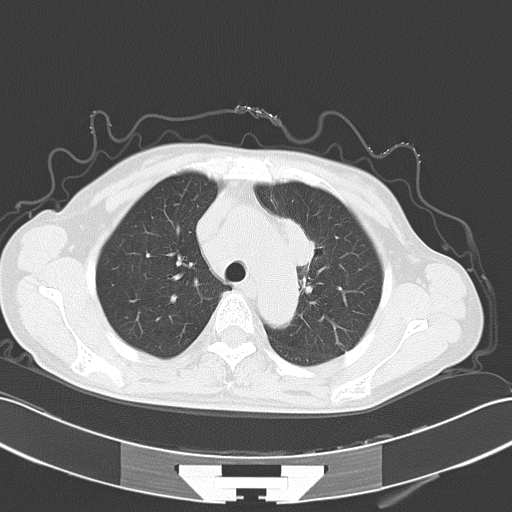
Chest CT, one axial slice; slice 41 of 54 in the series (ordered by position); 120 kVp; lung window (W 1500 / L -600 HU); 5 mm slice thickness; 512 × 512 image matrix, field of view 353 × 353 mm. Patient: female, 50 years. Case-level facts recorded for this patient, not image findings: clinical TNM (as recorded): T2a N1 M1c.
Structures marked on this image (rectangle marked by the reading radiologist):
- lung tumour (recorded histology: adenocarcinoma): bounding box (x1, y1, x2, y2) in pixels: (278, 206, 317, 272)